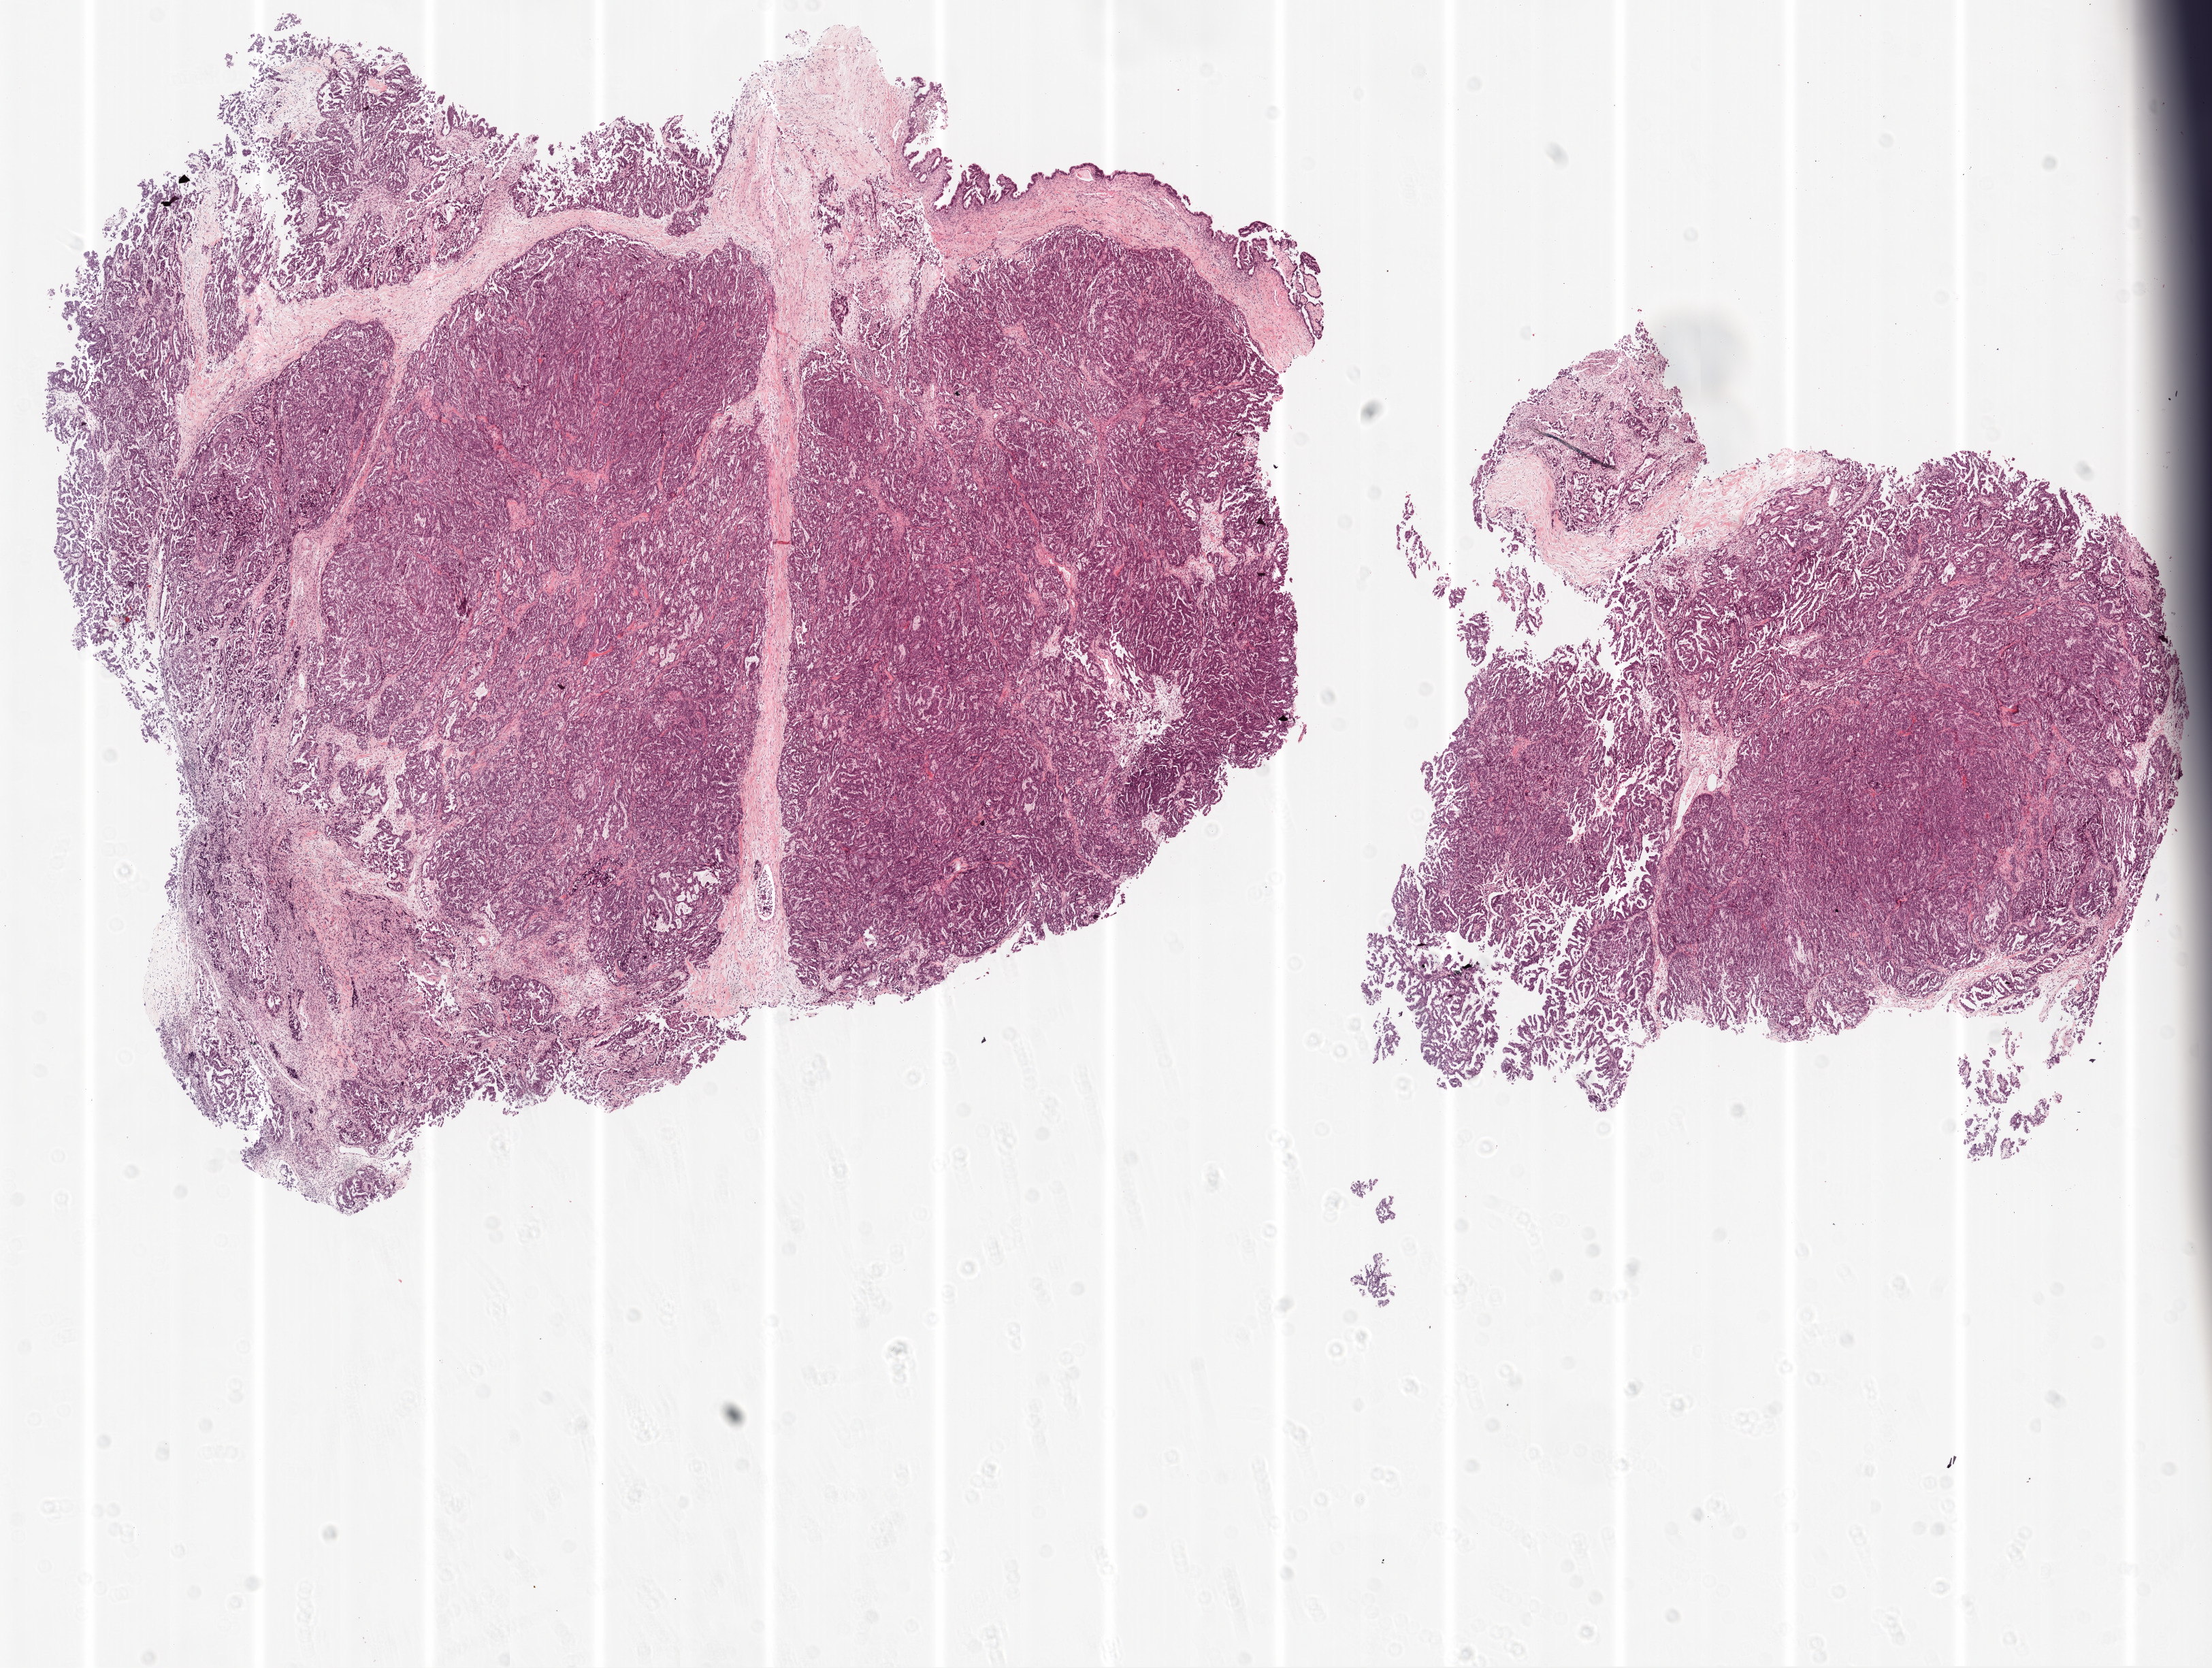
H&E-stained whole-slide image — low-resolution overview of the scanned area, about 13.0 x 9.8 mm (acquisition: 20x scan); frozen section from the top of the tissue portion; ovary, primary tumour sample. Patient: female, age at initial diagnosis 62 years. Histologic grade: G3 (poorly differentiated). Pathologist review of this section (percent, as recorded): tumour cells 80%, tumour nuclei 80%, normal cells 0%, stromal cells 20%, necrosis 0%. Inflammatory infiltration, as recorded: lymphocyte infiltration 0%, monocyte infiltration 0%, neutrophil infiltration 0%.
- histologic diagnosis: Serous cystadenocarcinoma, NOS
- FIGO stage: IIIC